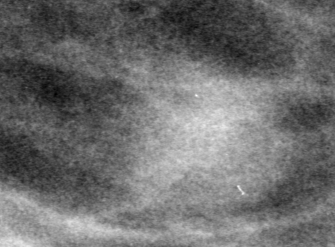
Region of interest cut from a scanned film mammogram (one marked finding), left breast, MLO view, BI-RADS breast density category 1 (scale 1–4).
- Marked abnormality: mass, shape round, margins obscured; BI-RADS assessment category 0 (incomplete: needs additional imaging); pathology (as recorded): benign.